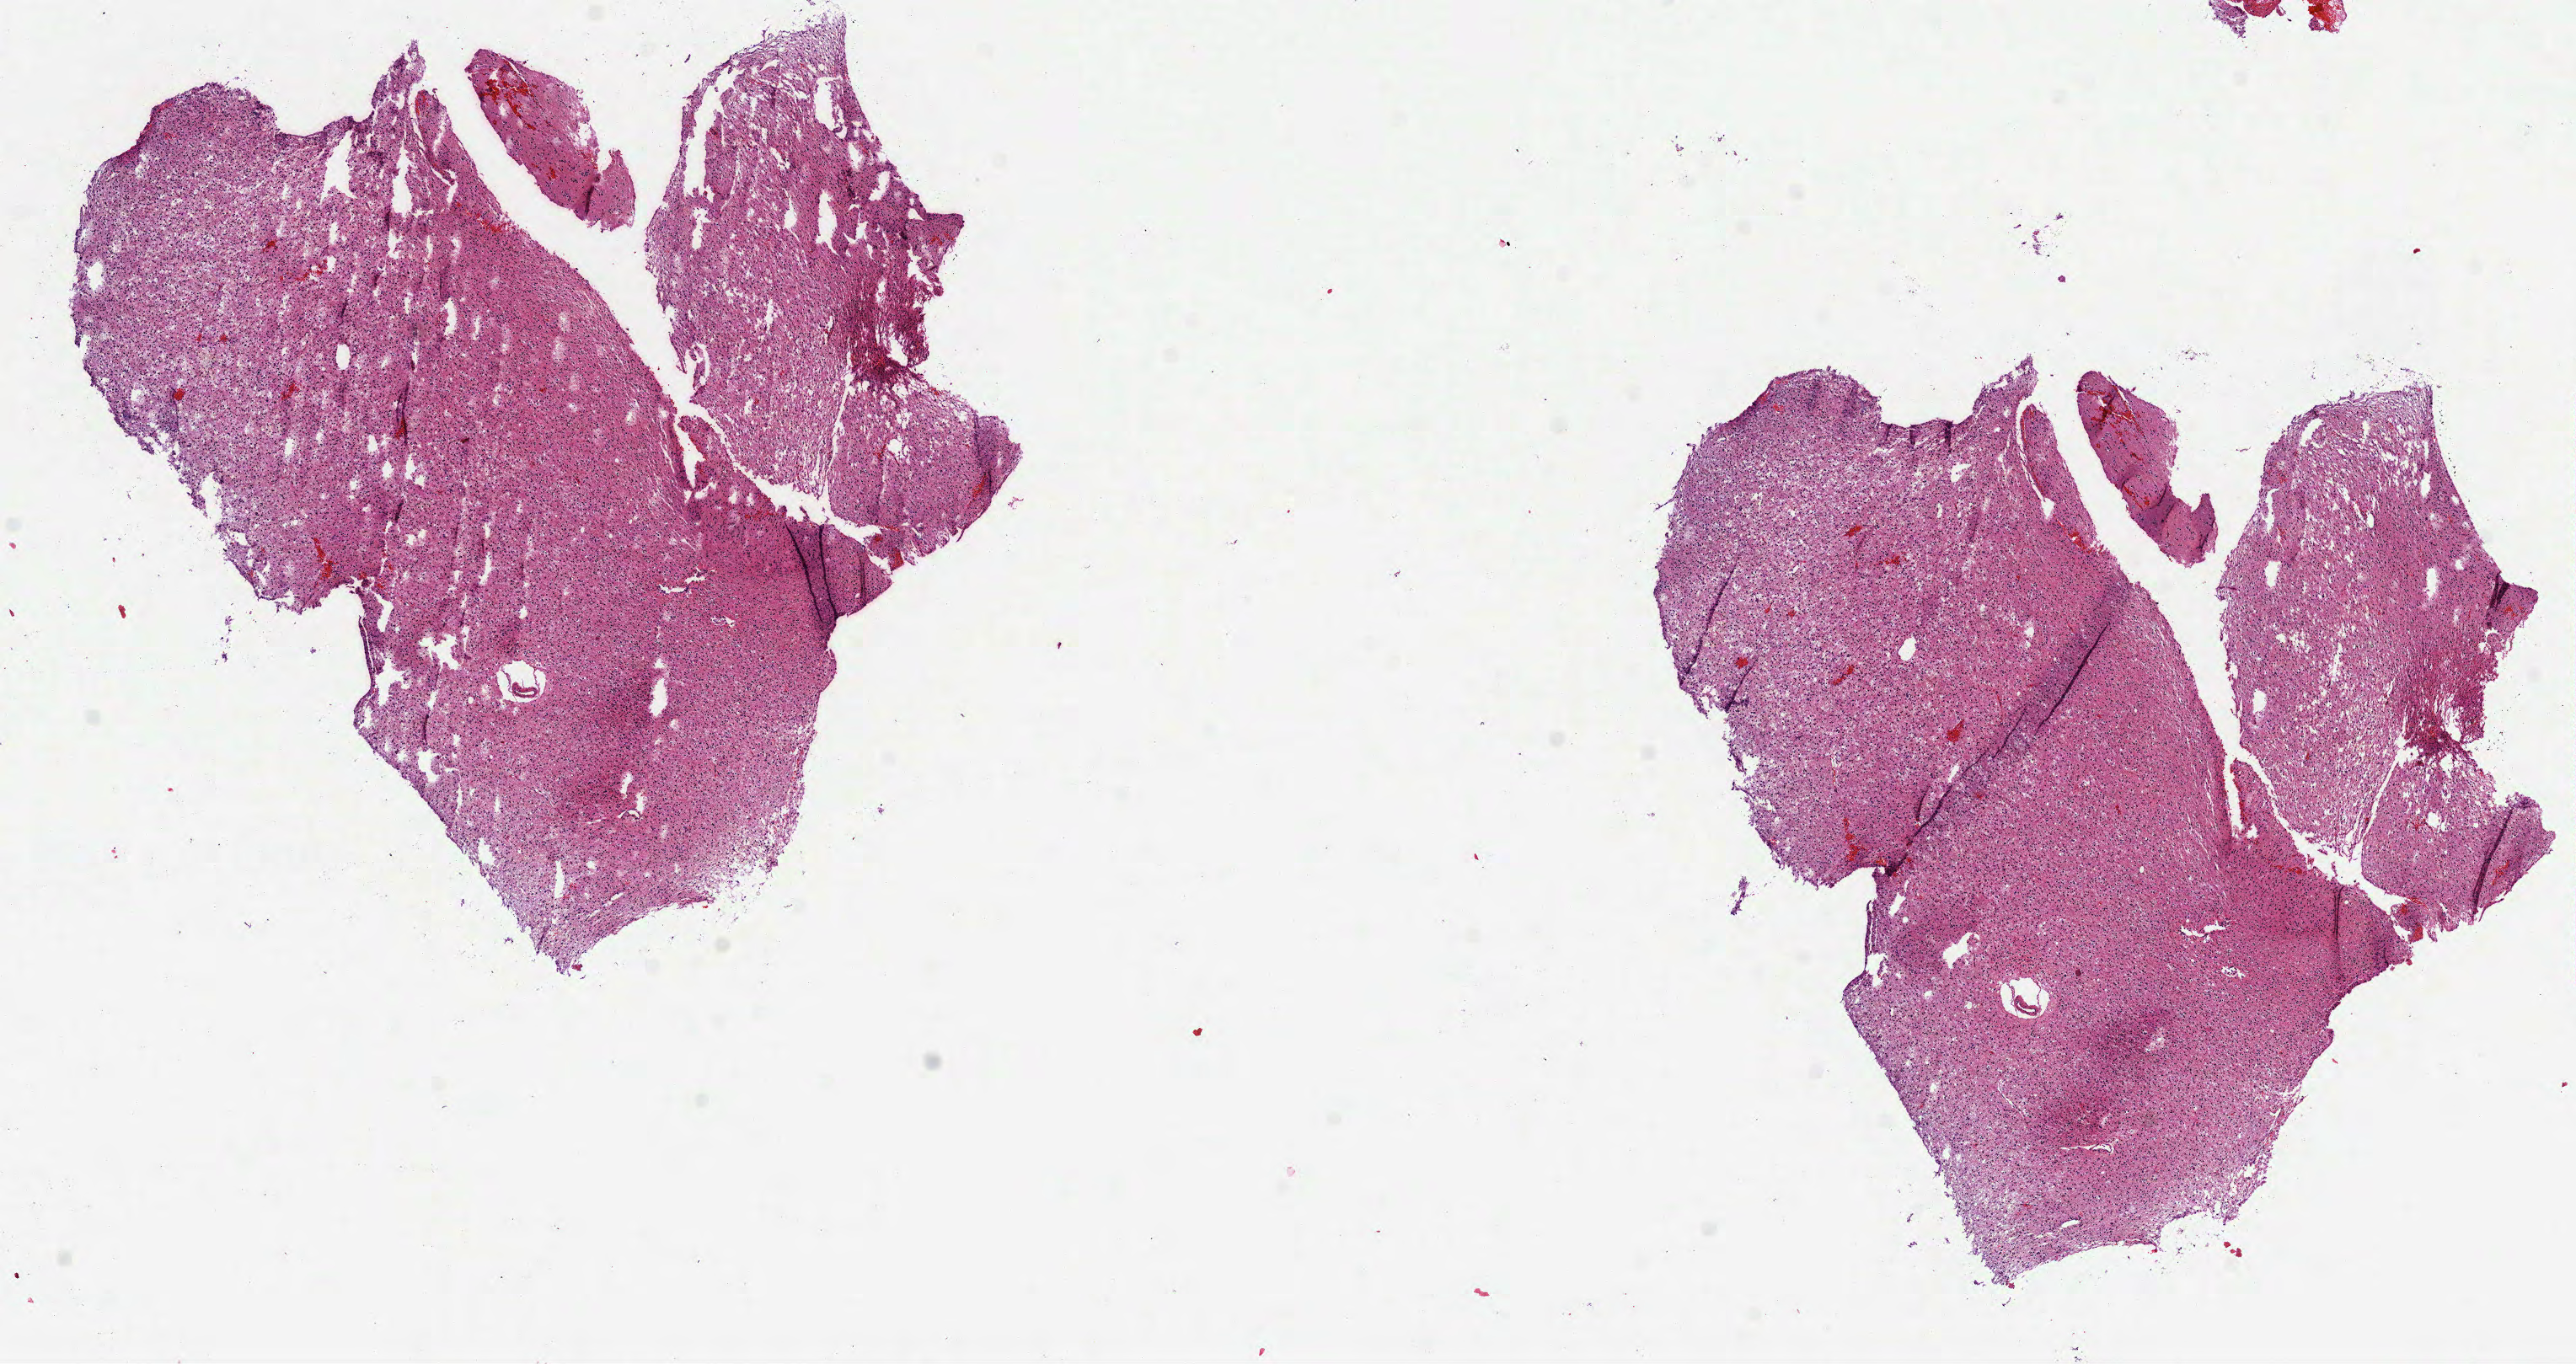
Digitized Hematoxylin and eosin (H&E) stained tissue section (whole slide), shown as a low-resolution overview of the whole scanned area (about 12.3 x 6.5 mm, from a 40x scan). FFPE section. Brain, primary tumour sample. Patient: female, age at initial diagnosis 44 years. Histologic grade: G3 (poorly differentiated).
Laterality: right. Pathologic diagnosis: Astrocytoma, anaplastic.